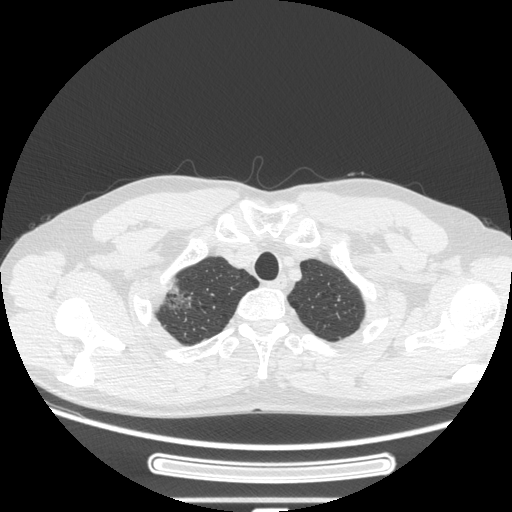
Chest CT, one axial slice. Position 236 of 269 along the scan axis. Lung window (W 1500 / L -600 HU). 1.25 mm slice thickness. 512 × 512 image matrix, field of view 382 × 382 mm. Patient: male, 53 years. Case-level facts recorded for this patient, not image findings: clinical TNM (as recorded): T1c N0 M0; histopathological grade: G2.
Structures marked on this image (rectangle marked by the reading radiologist):
- lung tumour (recorded histology: adenocarcinoma): bounding box [x1, y1, x2, y2] px = [151, 280, 195, 318]